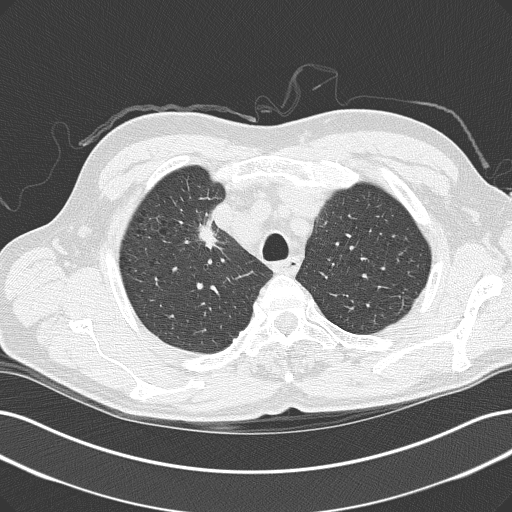
Chest CT (low-dose screening protocol), one axial image. Baseline annual screen. Lung window (W 1500 / L -600 HU). Lung (sharp) reconstruction kernel (B50f). 512 × 512 image matrix, field of view 365 × 365 mm. Male participant, aged 61 years at enrolment. Current smoker at enrolment.
- Expert-annotated lung lesion, bounding box <188,218,245,265> (left, top, right, bottom; pixels).
- The screening reader recorded 2 non-calcified nodules or masses ≥4 mm on this exam (right upper lobe, right upper lobe); which of them this box marks is not recorded.
- Official screen result: positive, change unspecified: nodule(s) >= 4 mm or enlarging nodule(s), mass(es), or other non-specific abnormalities suspicious for lung cancer.
- Lung cancer was diagnosed 54 days after this screen: adenocarcinoma, NOS, right upper lobe, poorly differentiated (G3), stage IIIB (AJCC 6th edition).